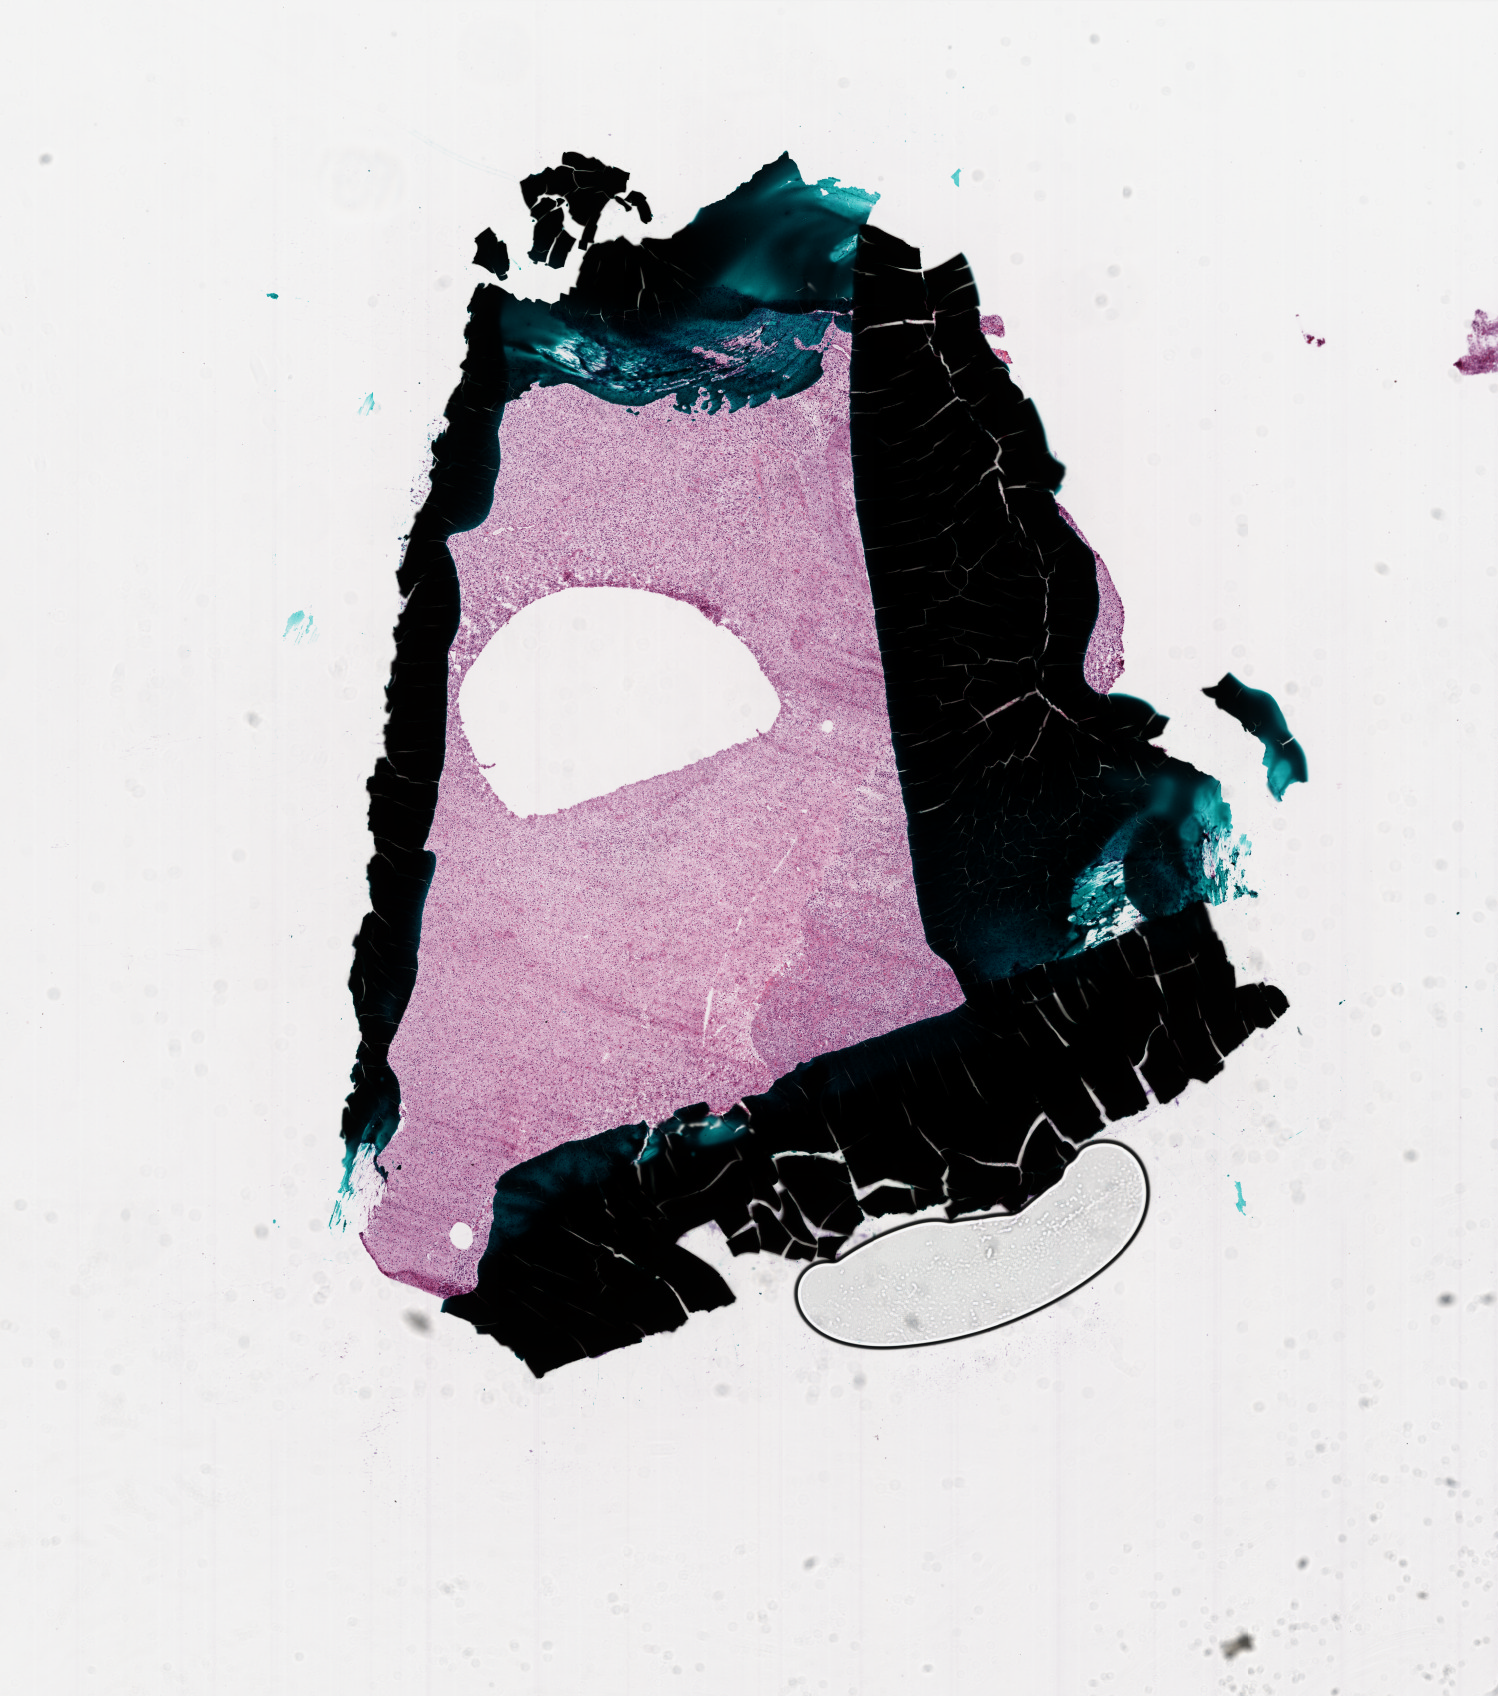
Digitized H&E-stained tissue section (whole slide), whole scanned area (about 12.0 x 13.6 mm, slide scanned at 20x) shown as a low-resolution overview; frozen section from the bottom of the tissue portion; primary tumour sample from the brain. Male, age 38 years at initial diagnosis. Composition of this section per pathologist review: tumour cells 100%, tumour nuclei 100%, normal cells 0%, stromal cells 0%, necrosis 0%.
Histologic diagnosis: Glioblastoma.